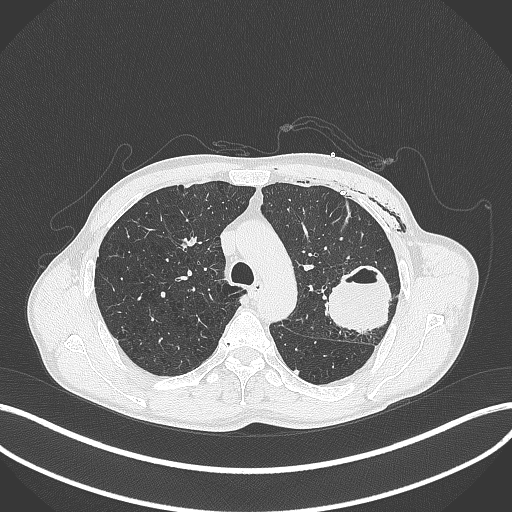
Chest CT, one axial slice. Position 288 of 457 along the scan axis. Reconstruction kernel B70f. Lung window (W 1500 / L -600 HU). 512 × 512 image matrix, field of view 400 × 400 mm. Patient: male, 58 years. Case-level facts recorded for this patient, not image findings: clinical TNM (as recorded): T3 N0 M0.
Structures marked on this image (rectangle marked by the reading radiologist):
- lung tumour (recorded histology: adenocarcinoma): bounding box [x1, y1, x2, y2] px = [318, 260, 394, 335]